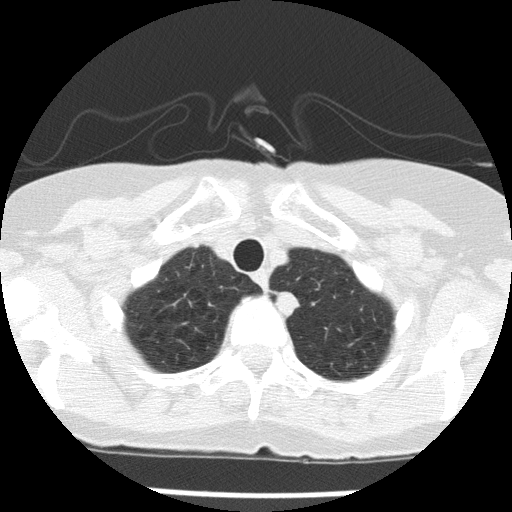
Low-dose screening chest CT, axial slice; baseline screening round; lung window (W 1500 / L -600 HU); 2 mm slice thickness; lung (sharp) reconstruction kernel (FC51); slice 17 of 143 in the series. Female, age 74 years at enrolment. Former smoker at enrolment.
Expert reader's lesion annotation, bounding box [x1, y1, x2, y2] px = [269, 288, 306, 318]. The screening reader recorded 2 non-calcified nodules or masses ≥4 mm on this exam (left lower lobe, left upper lobe); which of them this box marks is not recorded. Official screen result: positive, change unspecified: nodule(s) >= 4 mm or enlarging nodule(s), mass(es), or other non-specific abnormalities suspicious for lung cancer. Later outcome: lung cancer diagnosed 81 days after this screen — adenocarcinoma, NOS, left upper lobe, poorly differentiated (G3), stage IA (AJCC 6th edition), 24 mm at pathology.